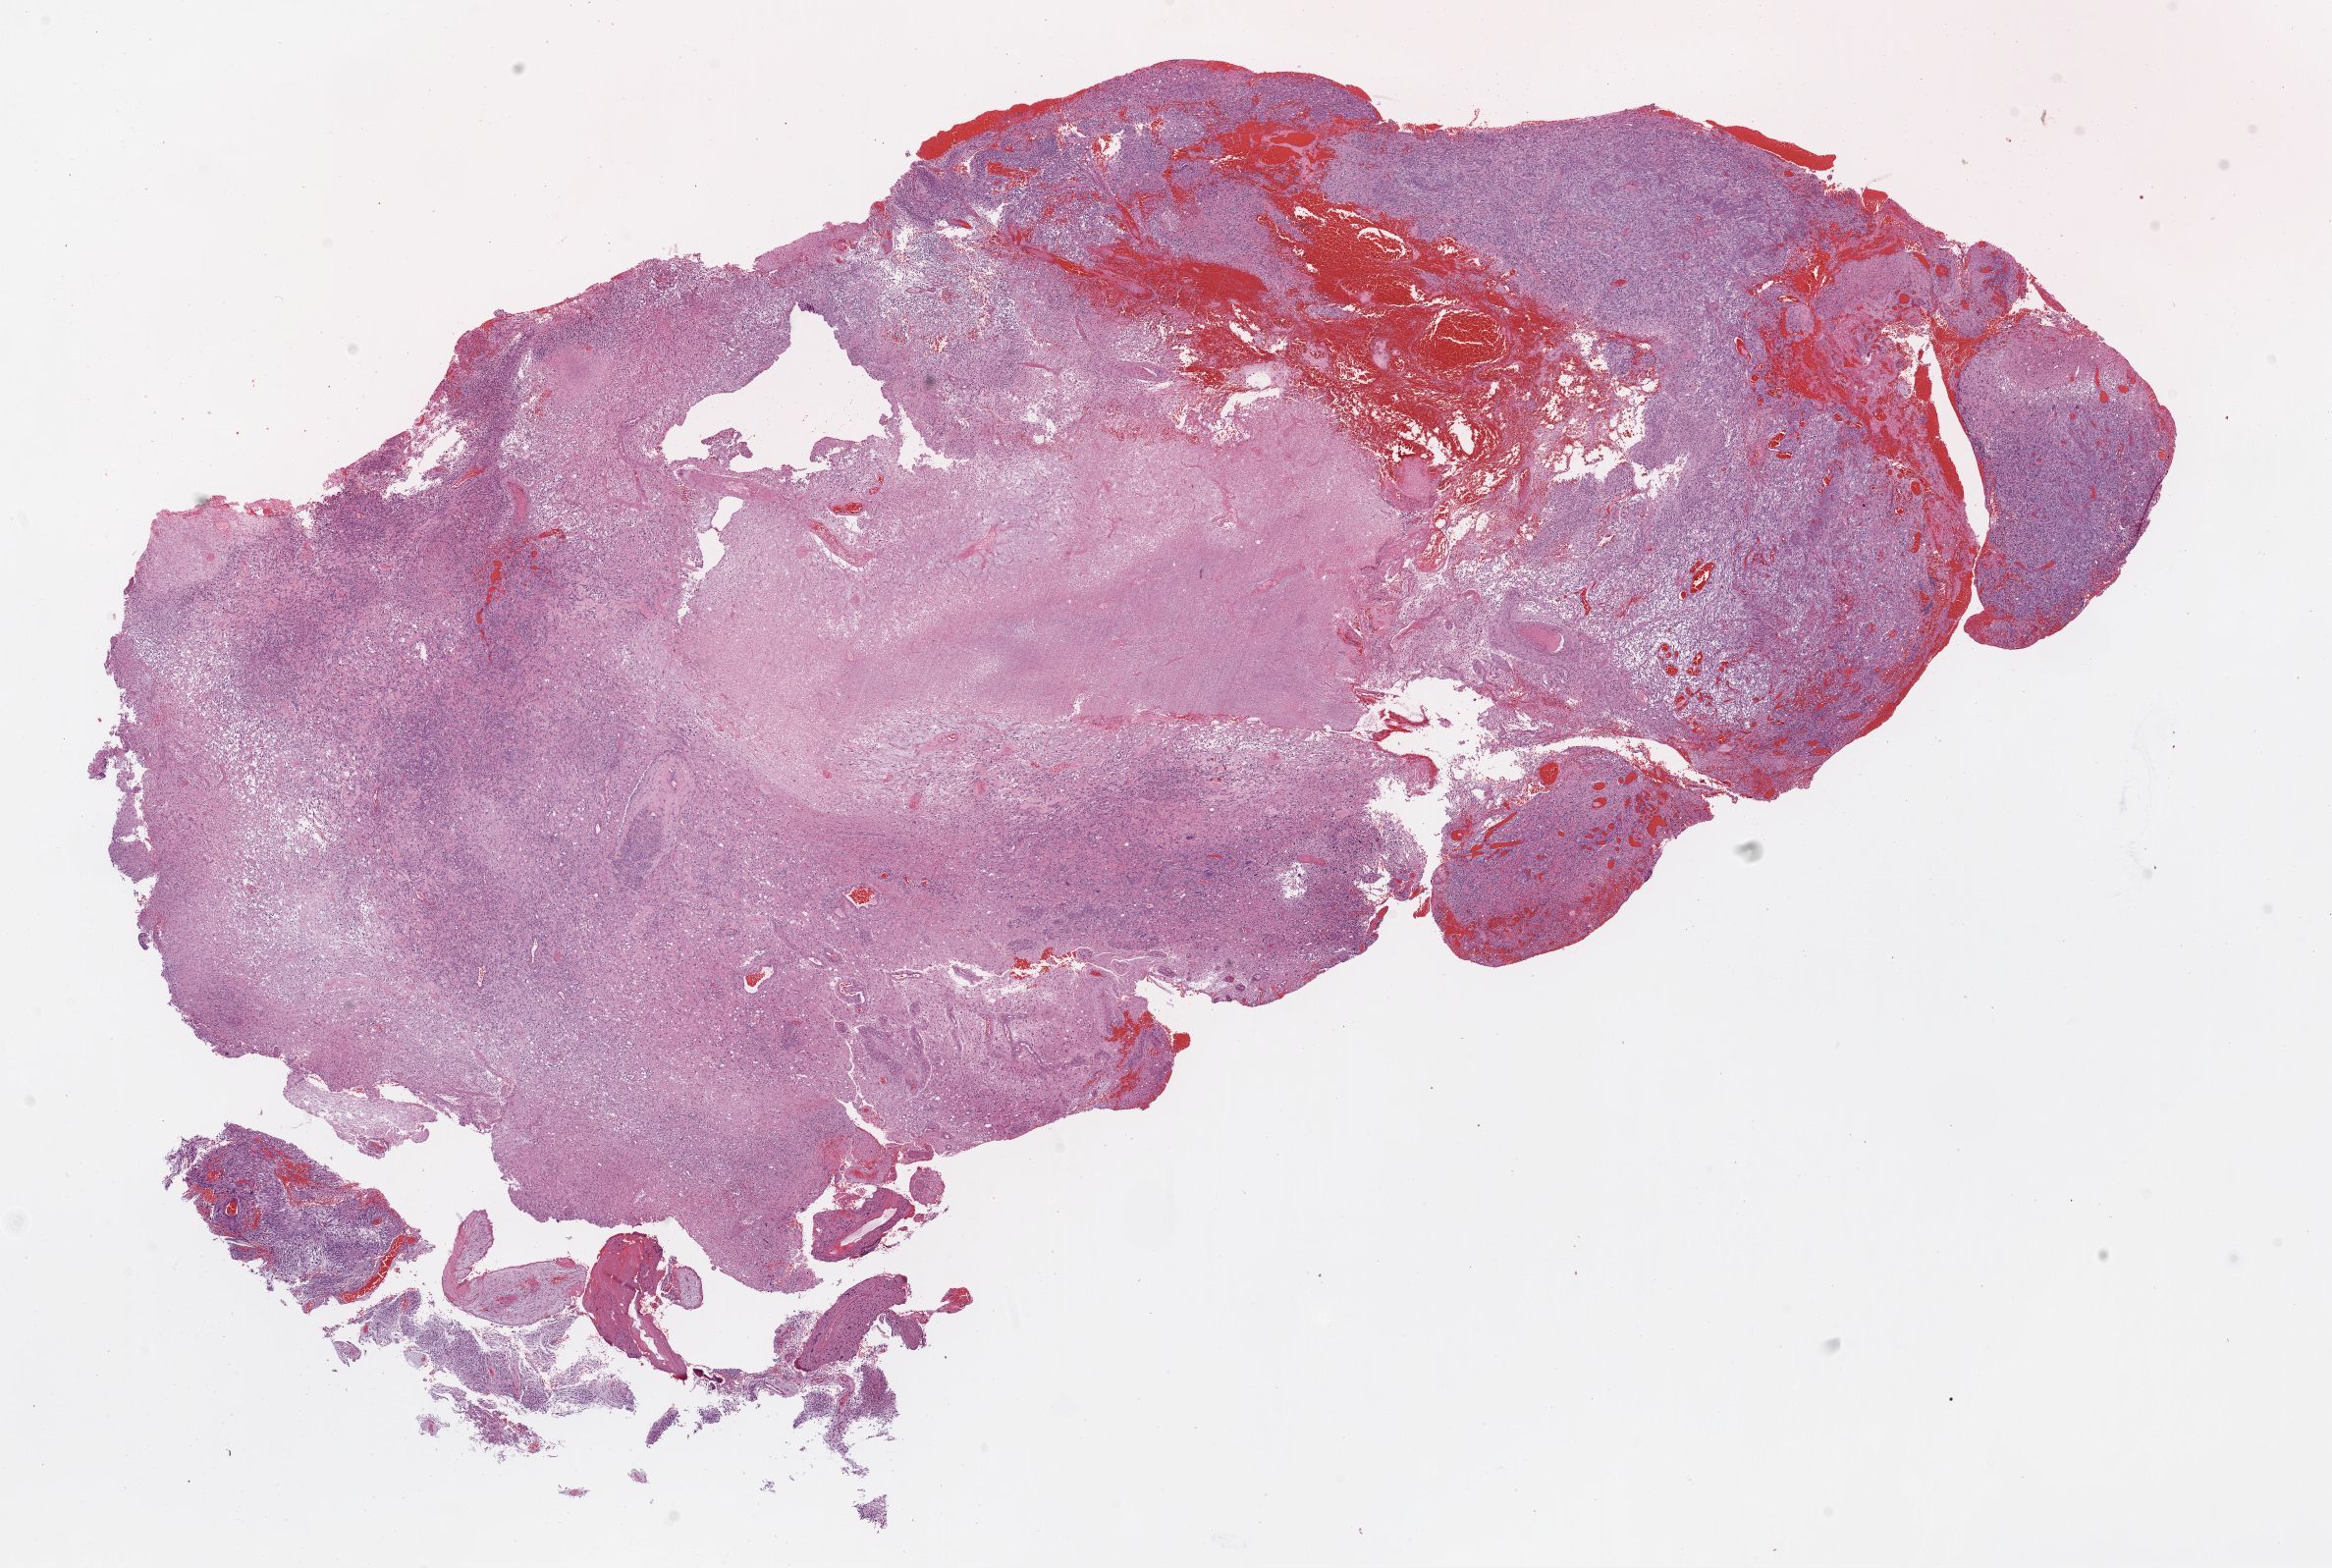
Digitized H&E tissue section (whole slide), low-resolution overview of the scanned area, about 19.1 x 12.8 mm; FFPE section; brain, primary tumour sample. Patient: male, age at initial diagnosis 62 years.
Diagnosis: Glioblastoma.